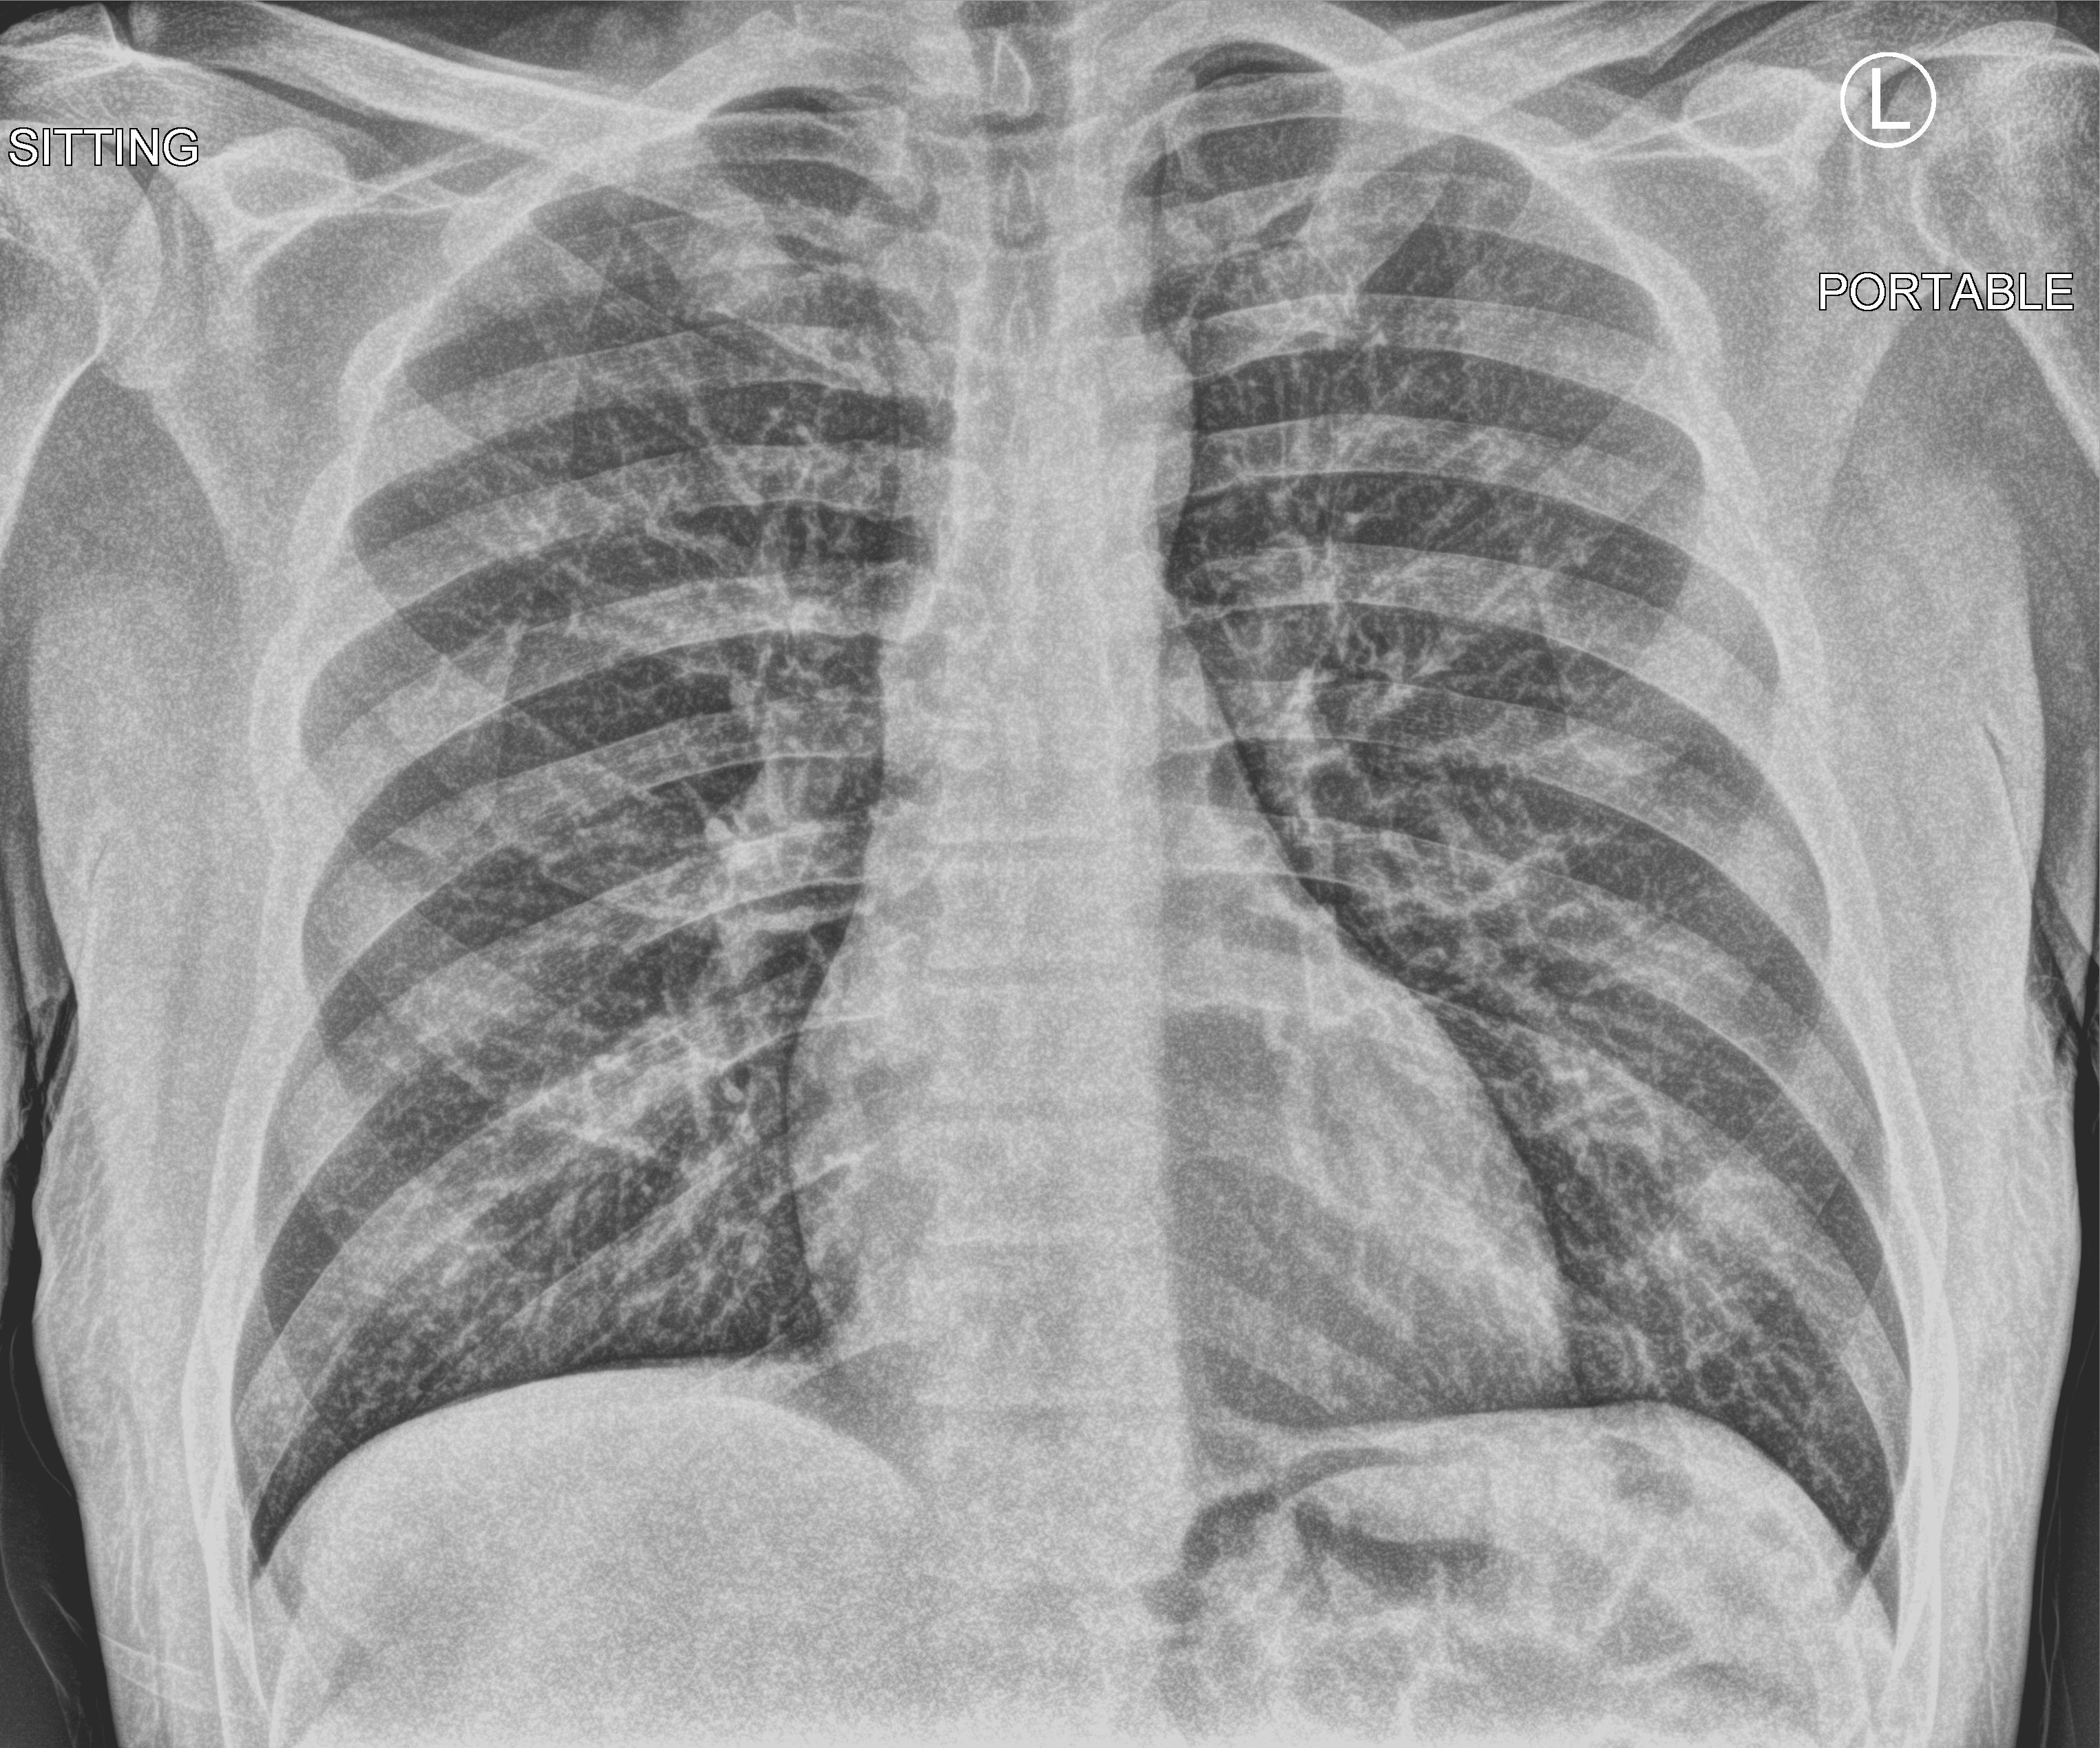
Bedside chest radiograph (computed radiography). Patient hospitalised with COVID-19; male, aged 18–59 years.
From the hospital-stay record, not from the radiograph (when in the stay this image was taken is not recorded):
- admitted to intensive care during this hospital stay: no